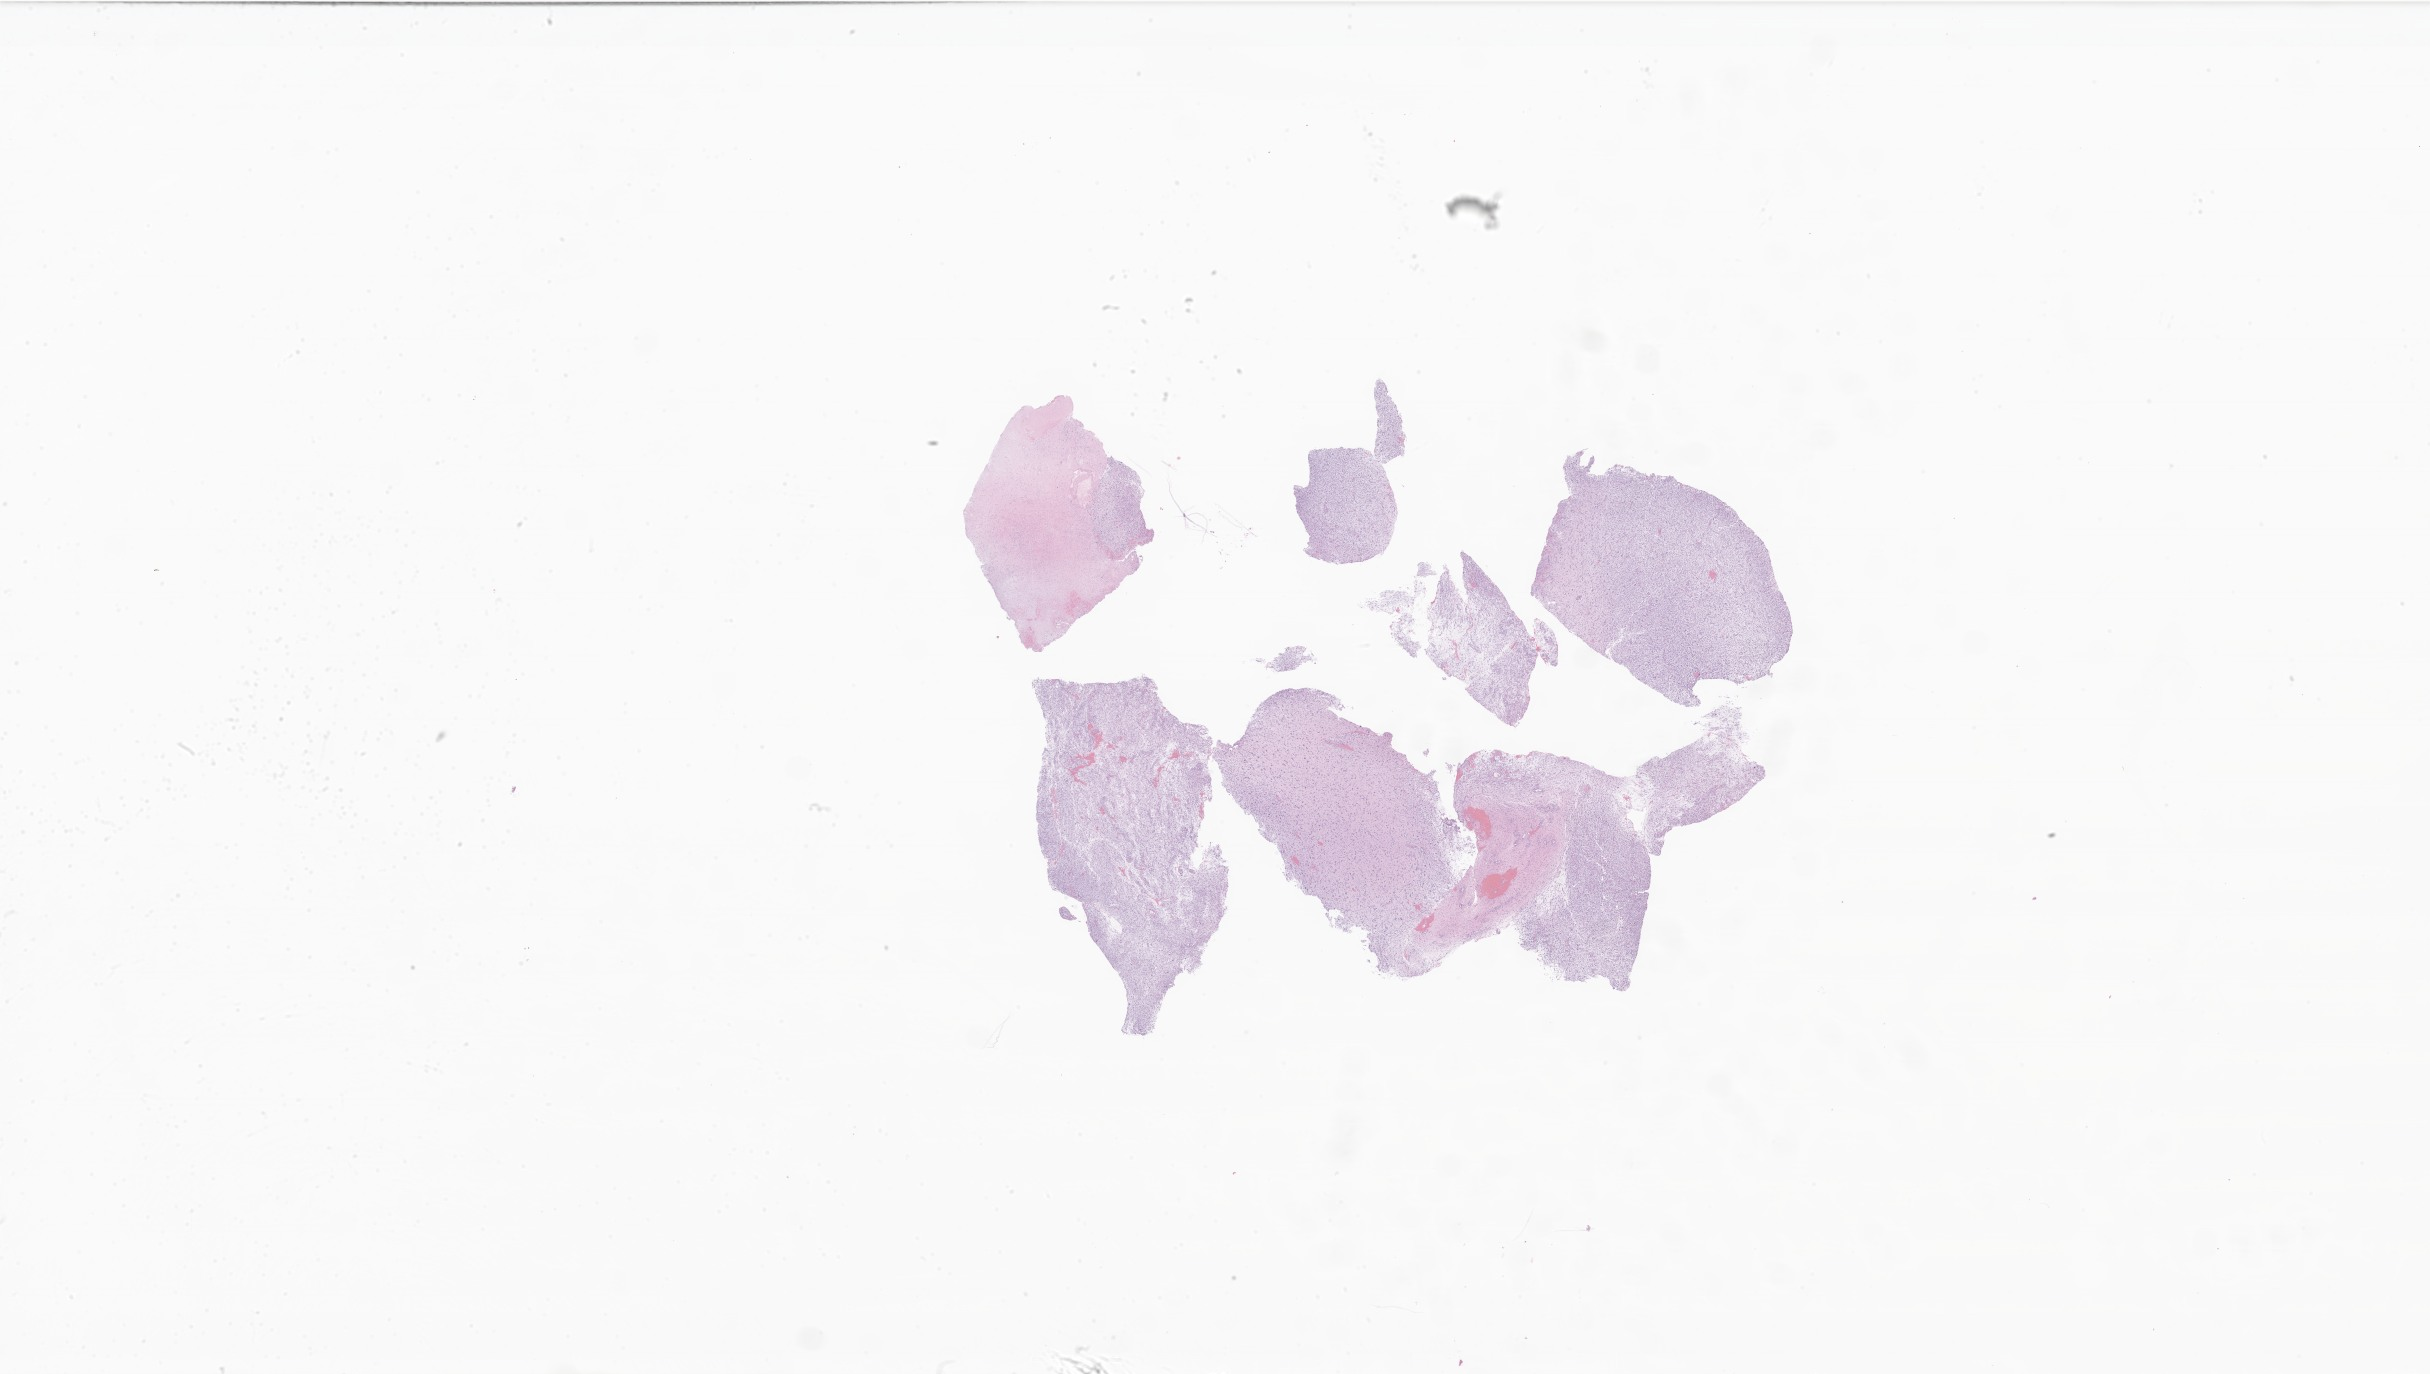
Hematoxylin and eosin (H&E) whole-slide image of tumor tissue from the brain, low-resolution overview of the scanned area, about 41.0 x 23.2 mm, formalin-fixed paraffin-embedded section. Patient: male, age 175 months (14 years 7 months).
• recorded diagnosis: Glioma, malignant